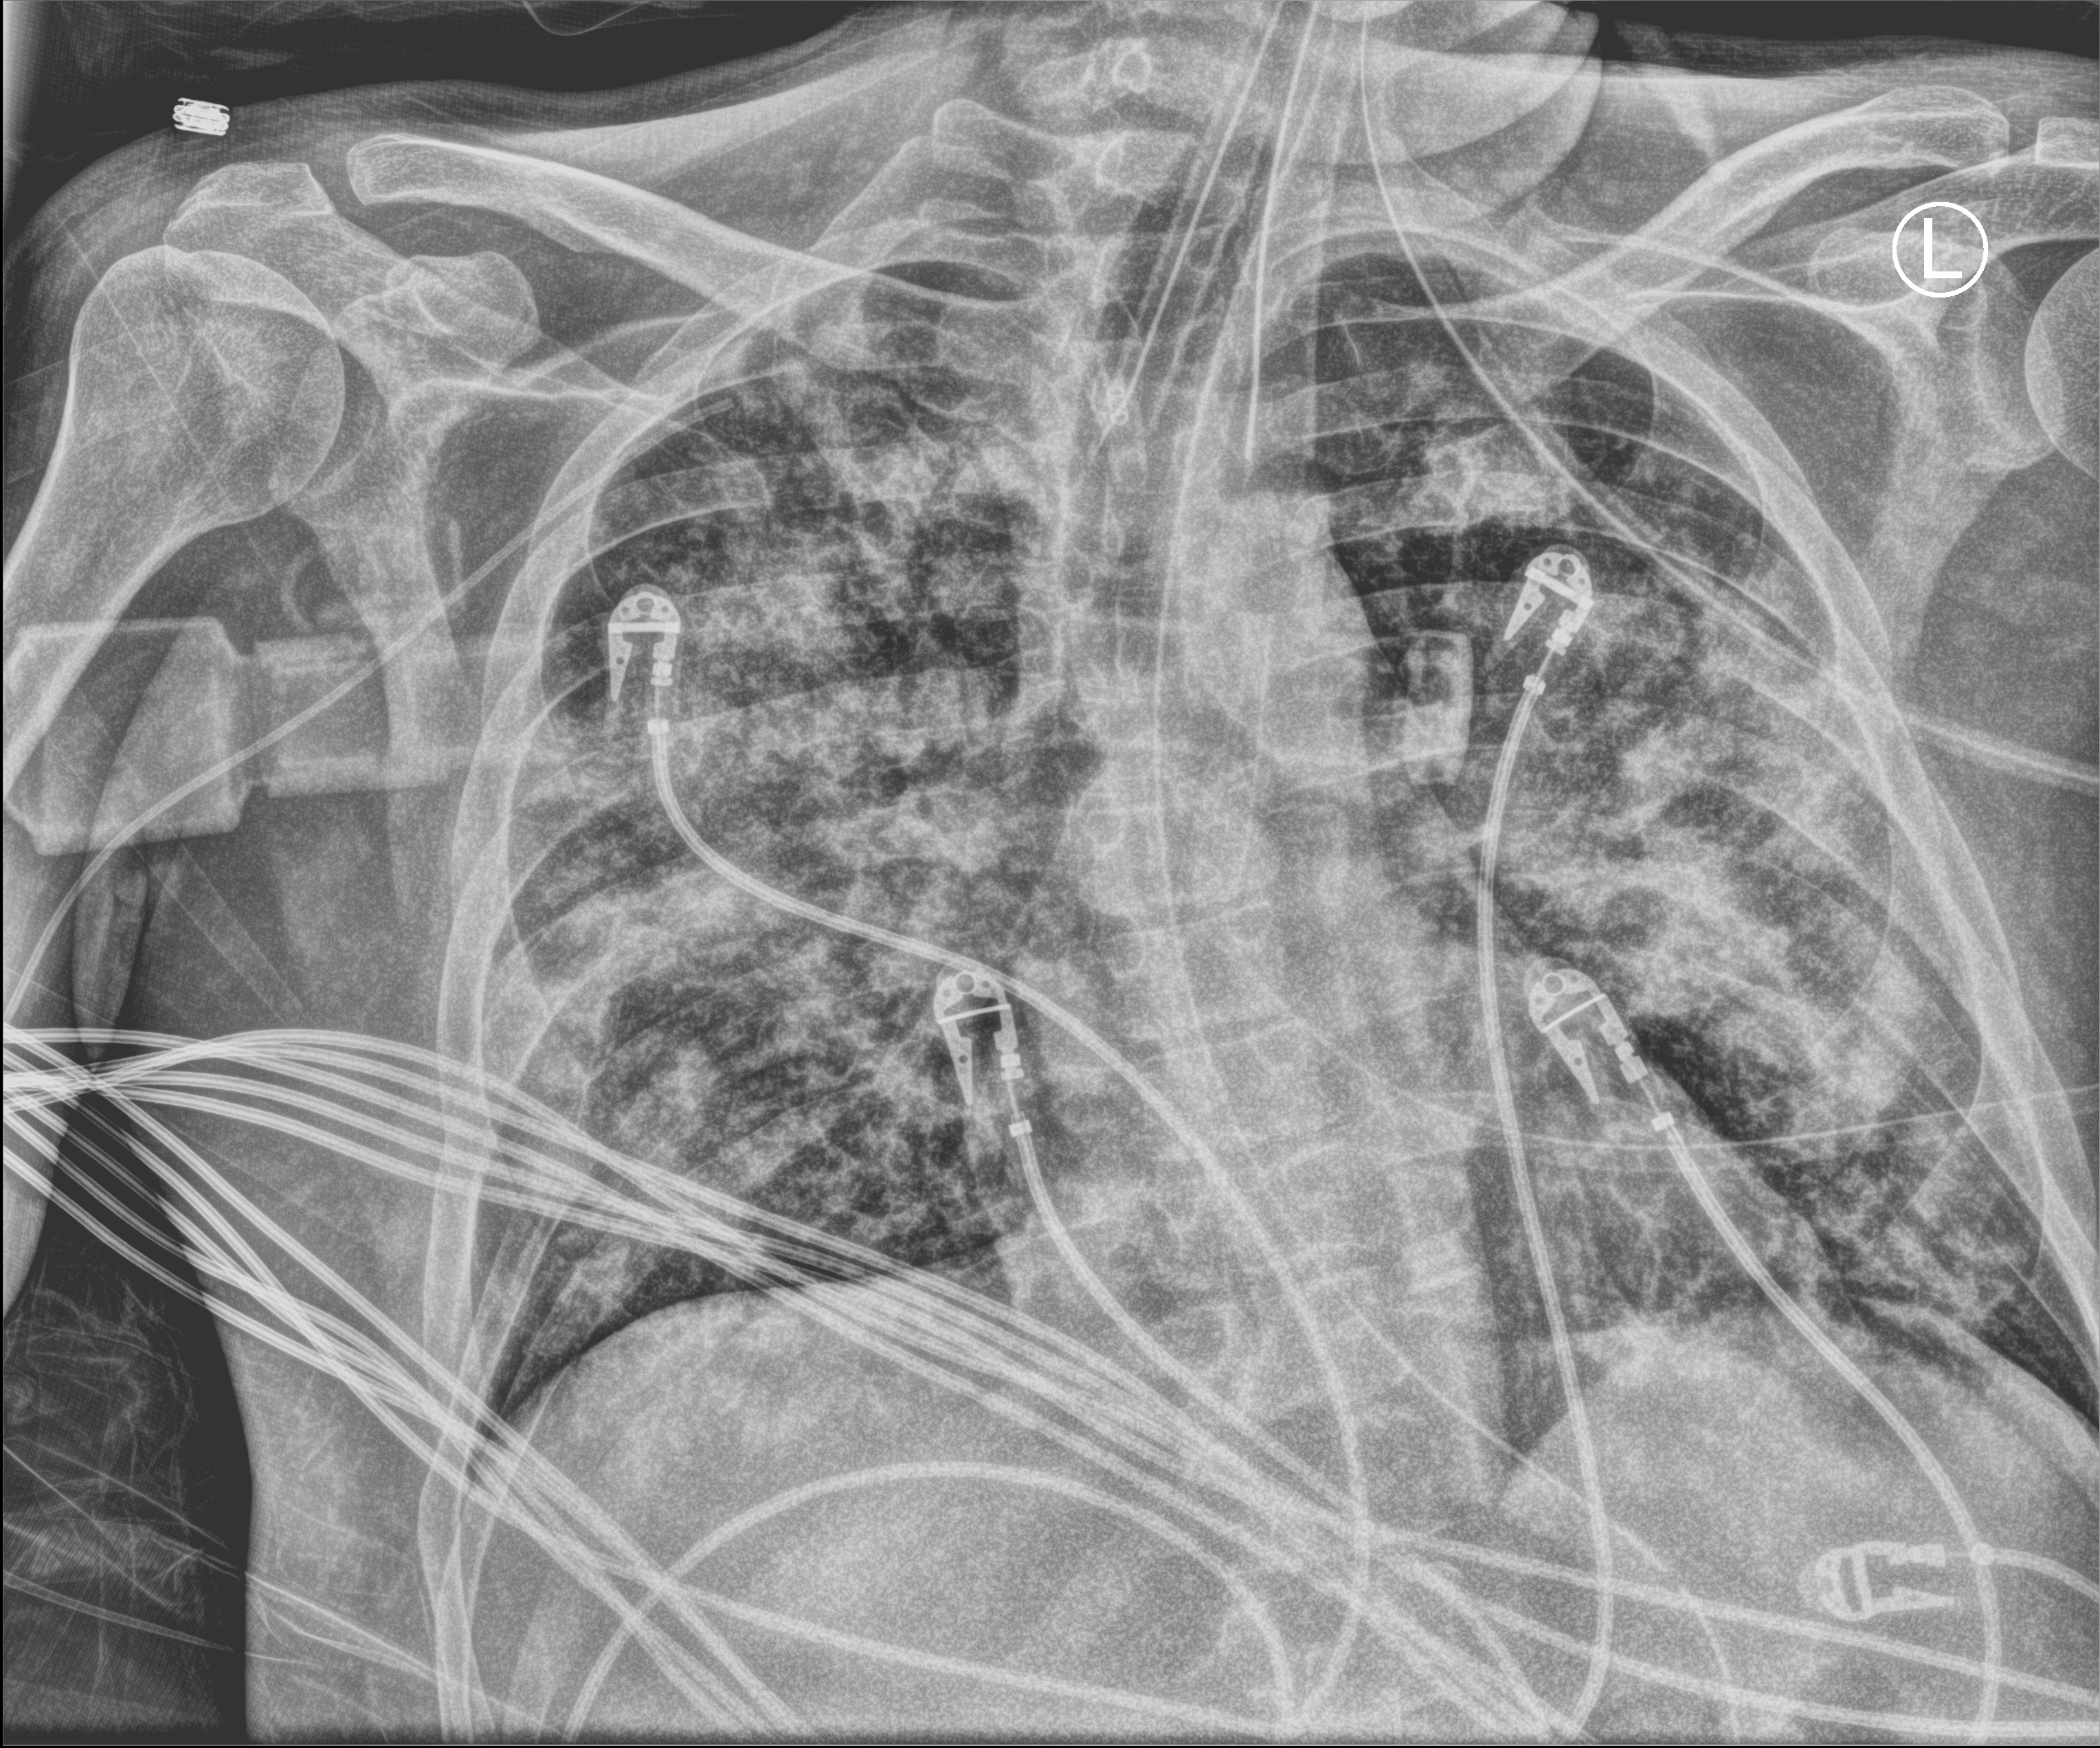
Portable chest radiograph; anteroposterior (AP) projection. Patient hospitalised with COVID-19; male, aged 18–59 years.
From the hospital-stay record, not from the radiograph (when in the stay this image was taken is not recorded): admitted to intensive care during this hospital stay: yes; other chronic lung disease (admission record): no; diabetes (admission record): yes.